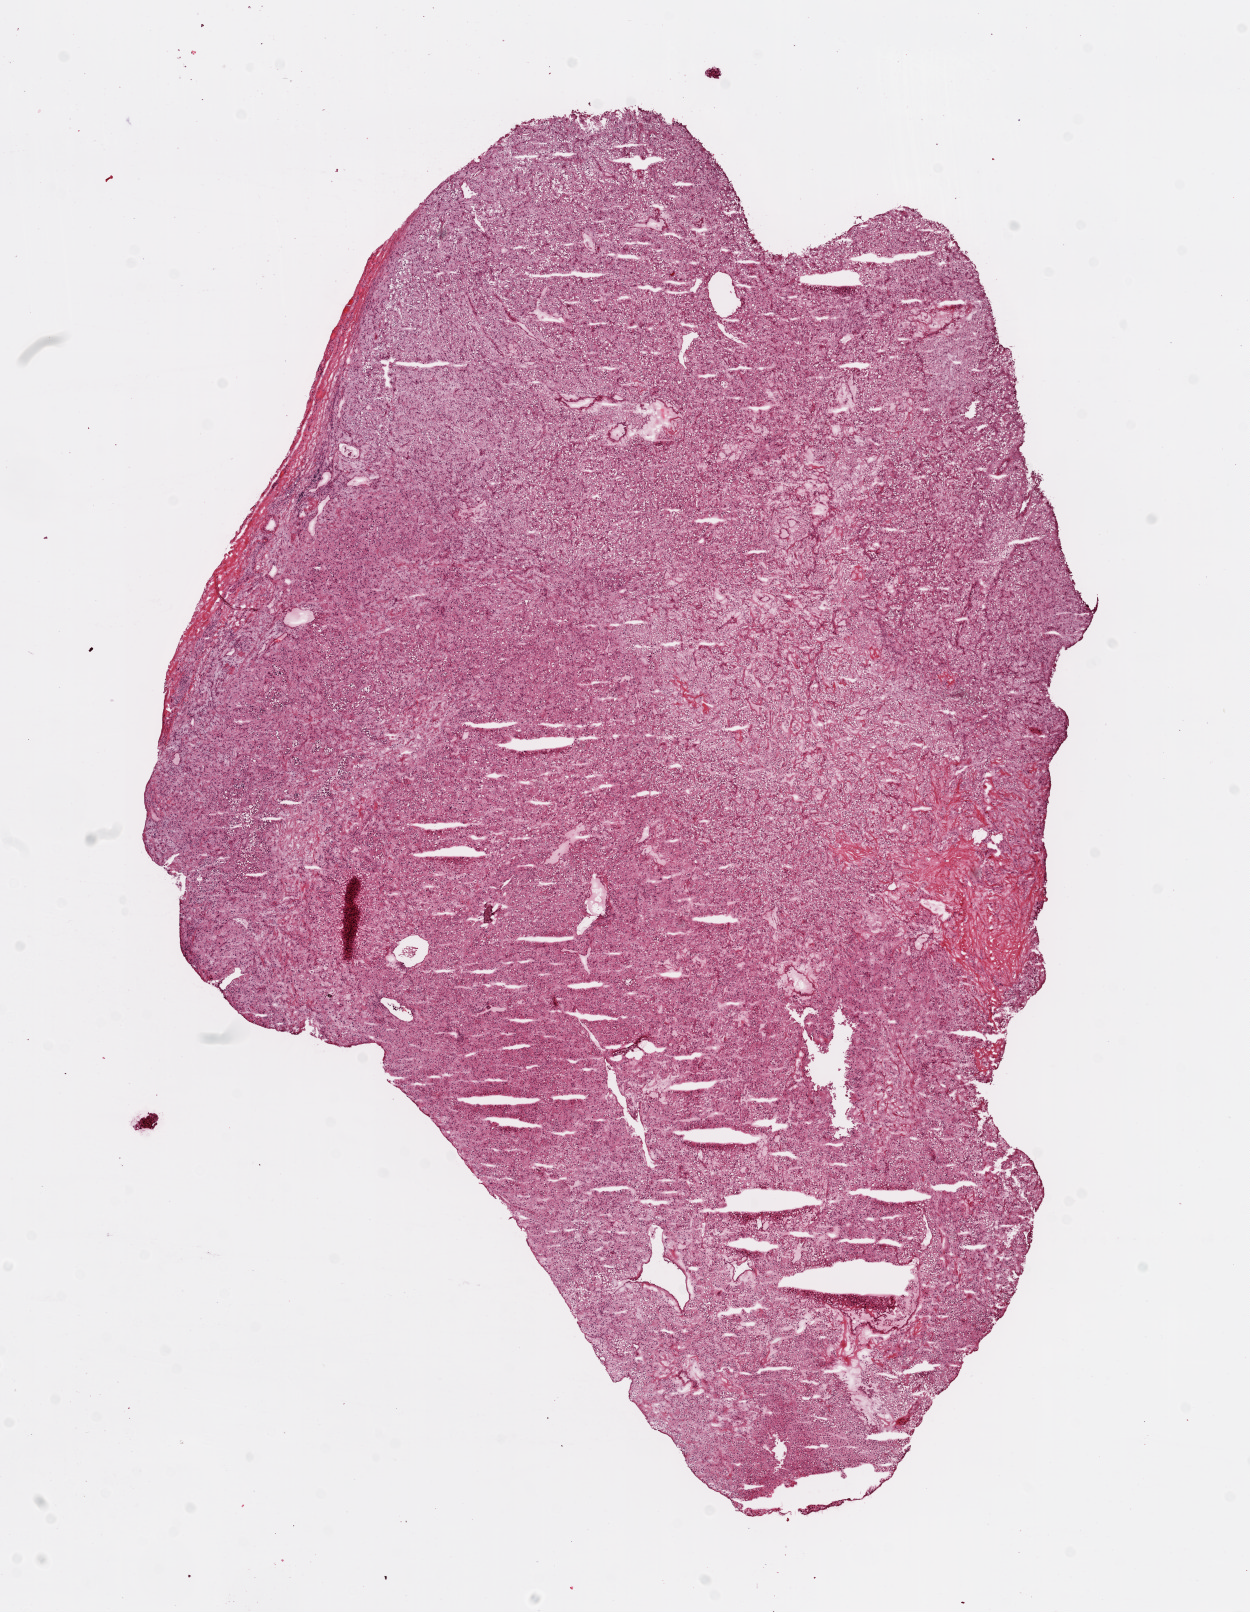
Digitized H&E-stained tissue section (whole slide), a low-resolution overview of the entire scanned area, about 10.0 x 12.9 mm (from a 20x scan), frozen section from the top of the tissue portion, kidney, primary tumour sample. Male patient; age at initial diagnosis 75 years. Histologic grade: G3 (poorly differentiated). Slide review estimates, as recorded: tumour cells 90%, tumour nuclei 85%, normal cells 0%, stromal cells 10%, necrosis 0%.
* AJCC pathologic stage: I
* lymph nodes positive (case pathology): 0 of 4 examined
* laterality: right
* pathologic diagnosis: Clear cell adenocarcinoma, NOS